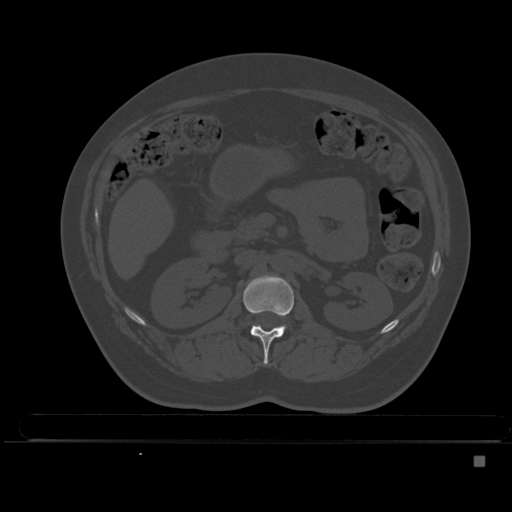
CT including the spine, one axial slice. Position 190 of 495 along the scan axis. Bone window (W 1800 / L 400 HU). 1.5 mm slice thickness. 512 × 512 image matrix, field of view 404 × 404 mm. Patient: female, 33 years. From the clinical record (not read from this slice): primary cancer: breast; vertebrae with lytic lesions (as recorded): T1.
Annotated regions visible in this slice (semi-automatically segmented with operator editing):
- L1 vertebra: bounding box (x1, y1, x2, y2) in pixels: (243, 275, 294, 364)